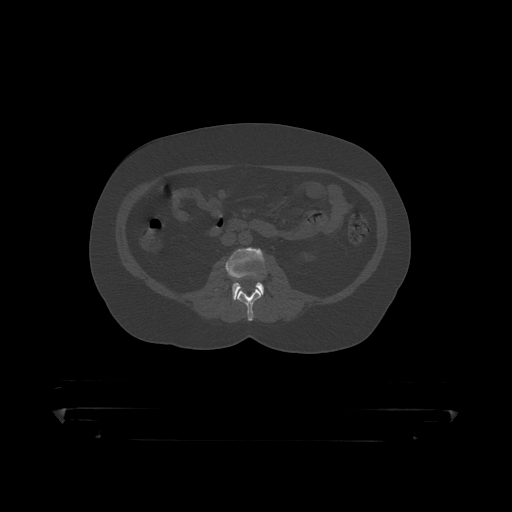
CT including the spine, one axial slice; slice 104 of 390 in the series (ordered by position); reconstruction kernel STANDARD; 120 kVp; bone window (W 1800 / L 400 HU); 1.25 mm slice thickness; 512 × 512 image matrix. Male patient, age 60 years. From the clinical record (not read from this slice): primary cancer: prostate.
Annotated regions visible in this slice (semi-automatically segmented with operator editing):
- L2 vertebra: box from (x=237, y=288) to (x=263, y=319) px
- L3 vertebra: (x=226, y=248)–(x=265, y=300)